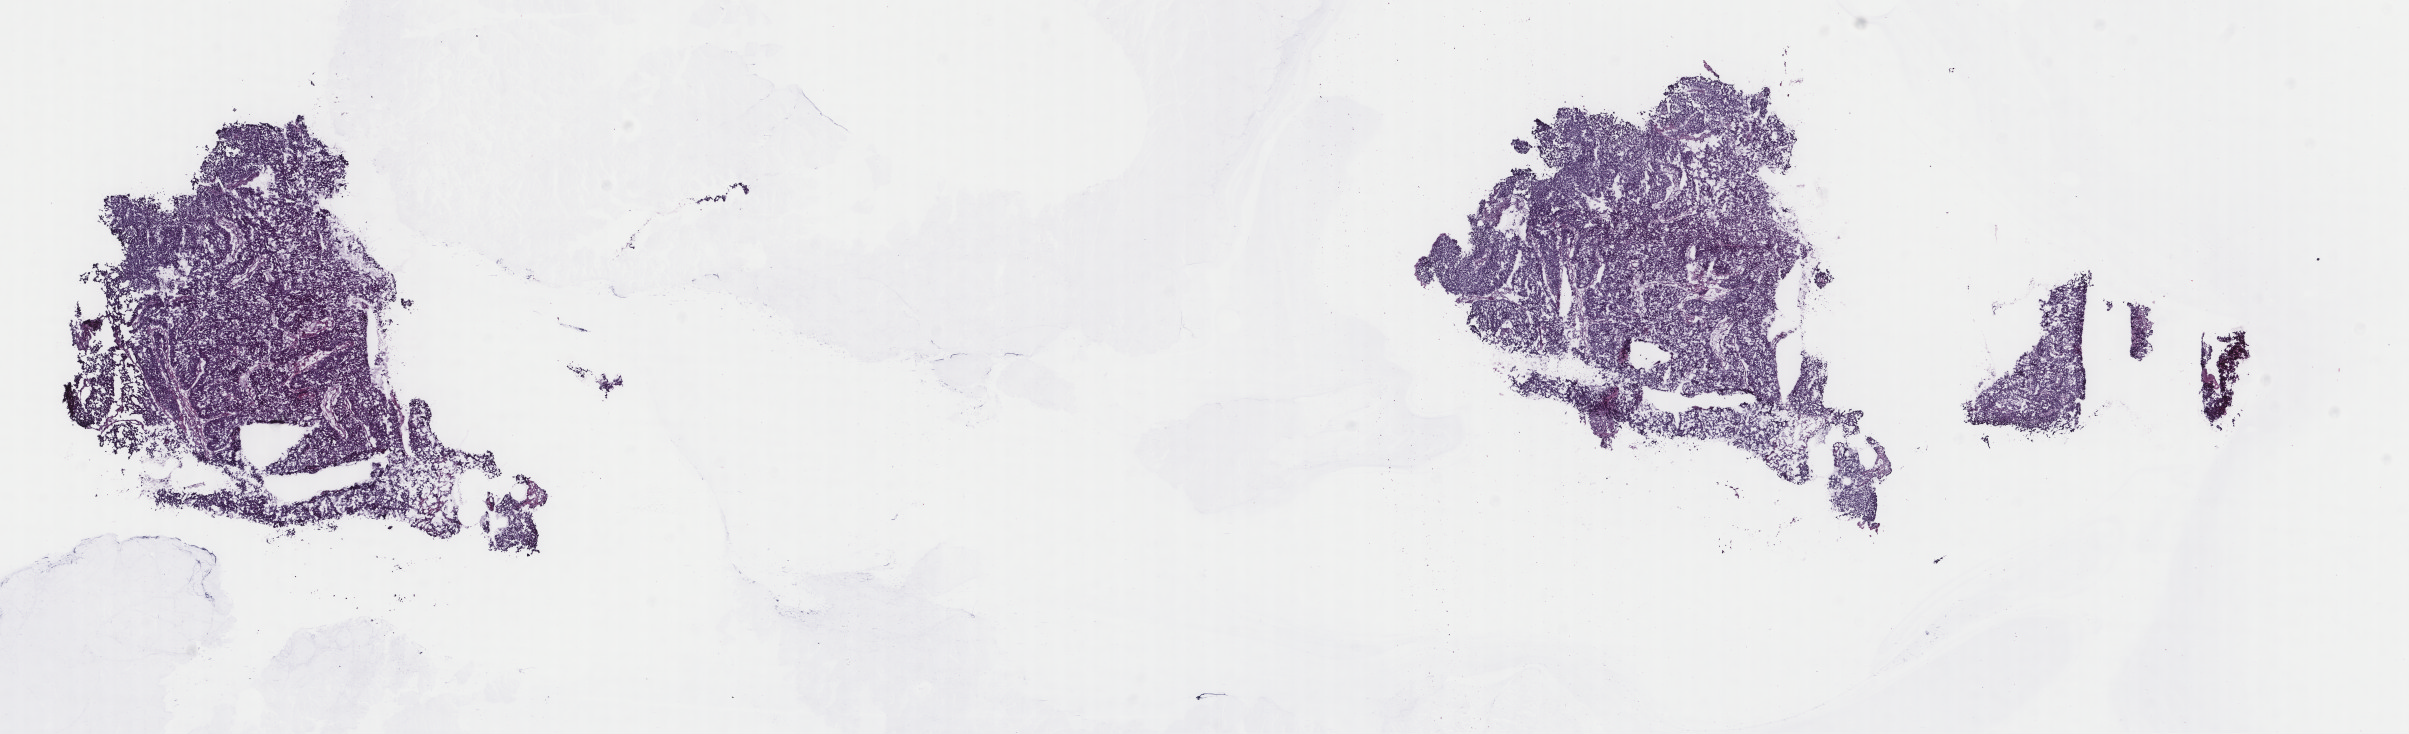
H&E-stained whole-slide image — low-resolution overview of the scanned area, about 19.1 x 5.8 mm, frozen section, sample: primary tumour, bladder. Male, age 47 years at initial diagnosis. Histologic grade: high grade. Pathologist review of this section (percent, as recorded): tumour cells 100%, tumour nuclei 90%, normal cells 0%, stromal cells 0%, necrosis 0%. Infiltration values recorded for this section: lymphocyte infiltration 2%, monocyte infiltration 0%, neutrophil infiltration 0%.
* pathologic diagnosis: Transitional cell carcinoma (posterior wall of bladder)
* AJCC pathologic stage: III (7th edition)
* lymph nodes positive (case pathology): 0 of 28 examined